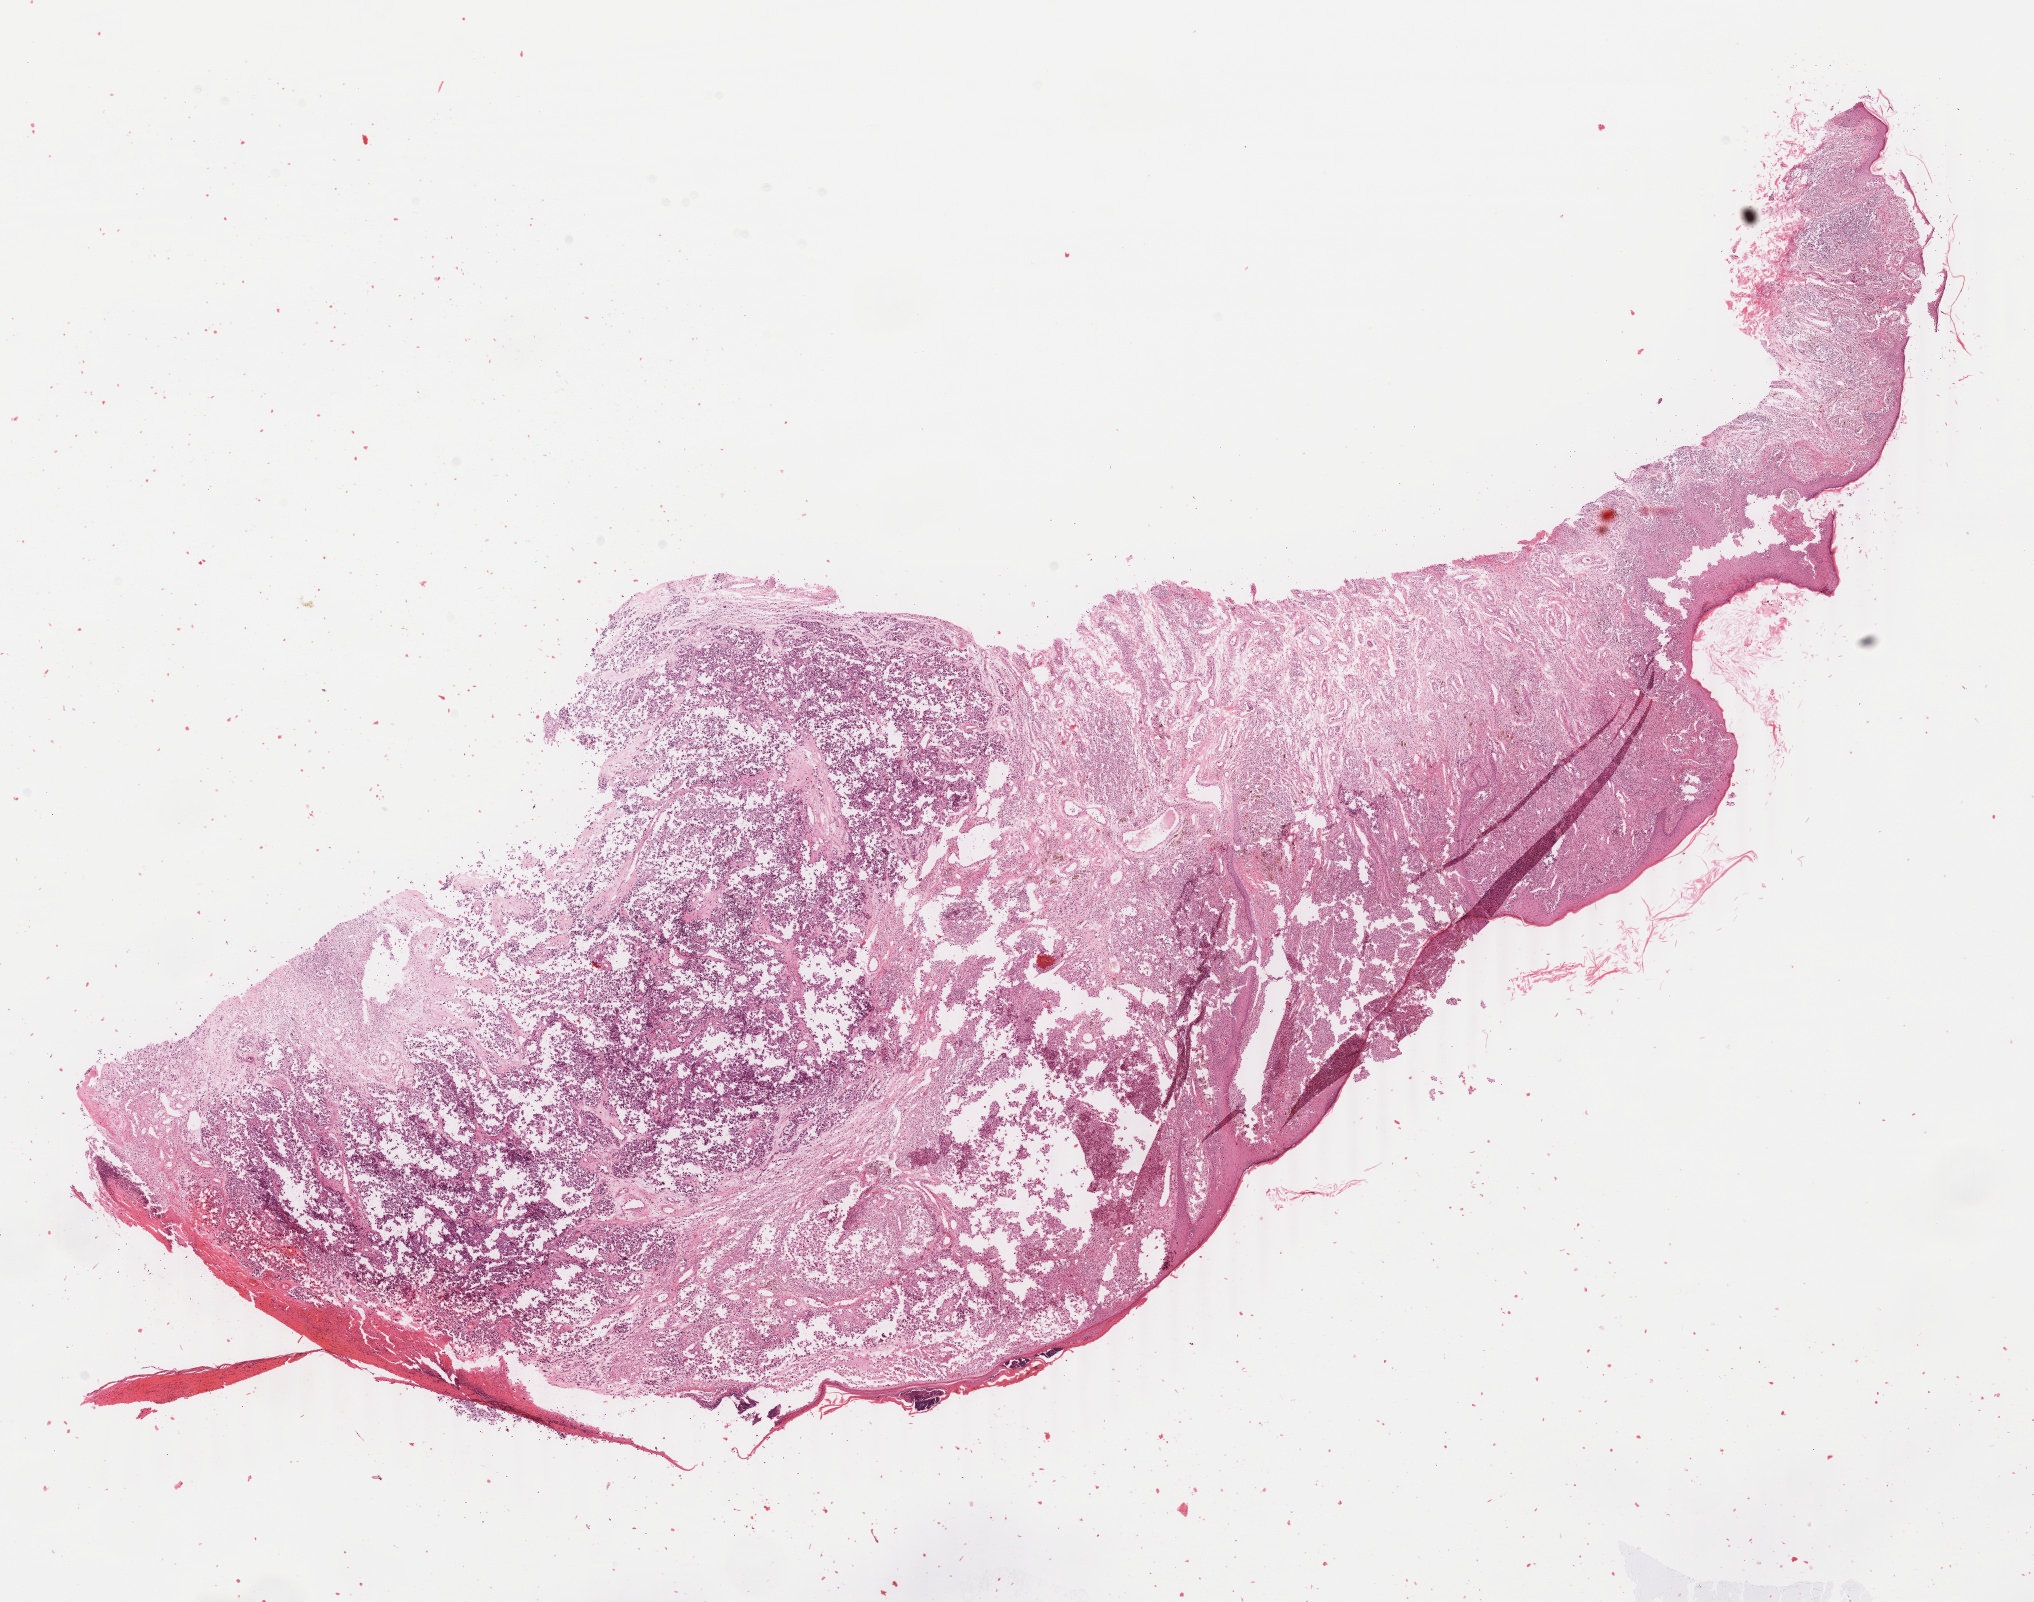
Whole-slide histology image, H&E, a low-resolution overview of the entire scanned area, about 16.2 x 12.7 mm; FFPE section; skin, primary tumour sample. Patient: male, age at initial diagnosis 63 years.
- histologic diagnosis: Nodular melanoma
- AJCC pathologic stage: IIA
- TNM: T2b N0 M0